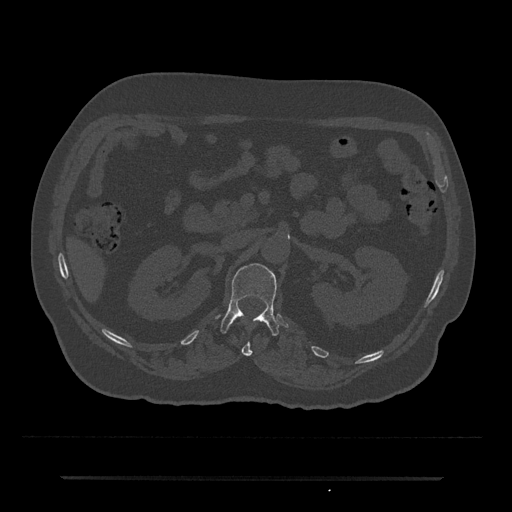
CT including the spine, one axial slice; position 83 of 797 along the scan axis; reconstruction kernel Br40s/3; bone window (W 1800 / L 400 HU); 0.5 mm slice thickness; 512 × 512 image matrix, field of view 437 × 437 mm. Male patient, age 69 years. From the clinical record (not read from this slice): primary cancer: prostate.
Annotated regions visible in this slice (semi-automatic segmentation, software-assisted and operator-edited):
- L1 vertebra: bounding box [x1, y1, x2, y2] px = [220, 263, 279, 336]
- T12 vertebra: [241, 341, 252, 356]